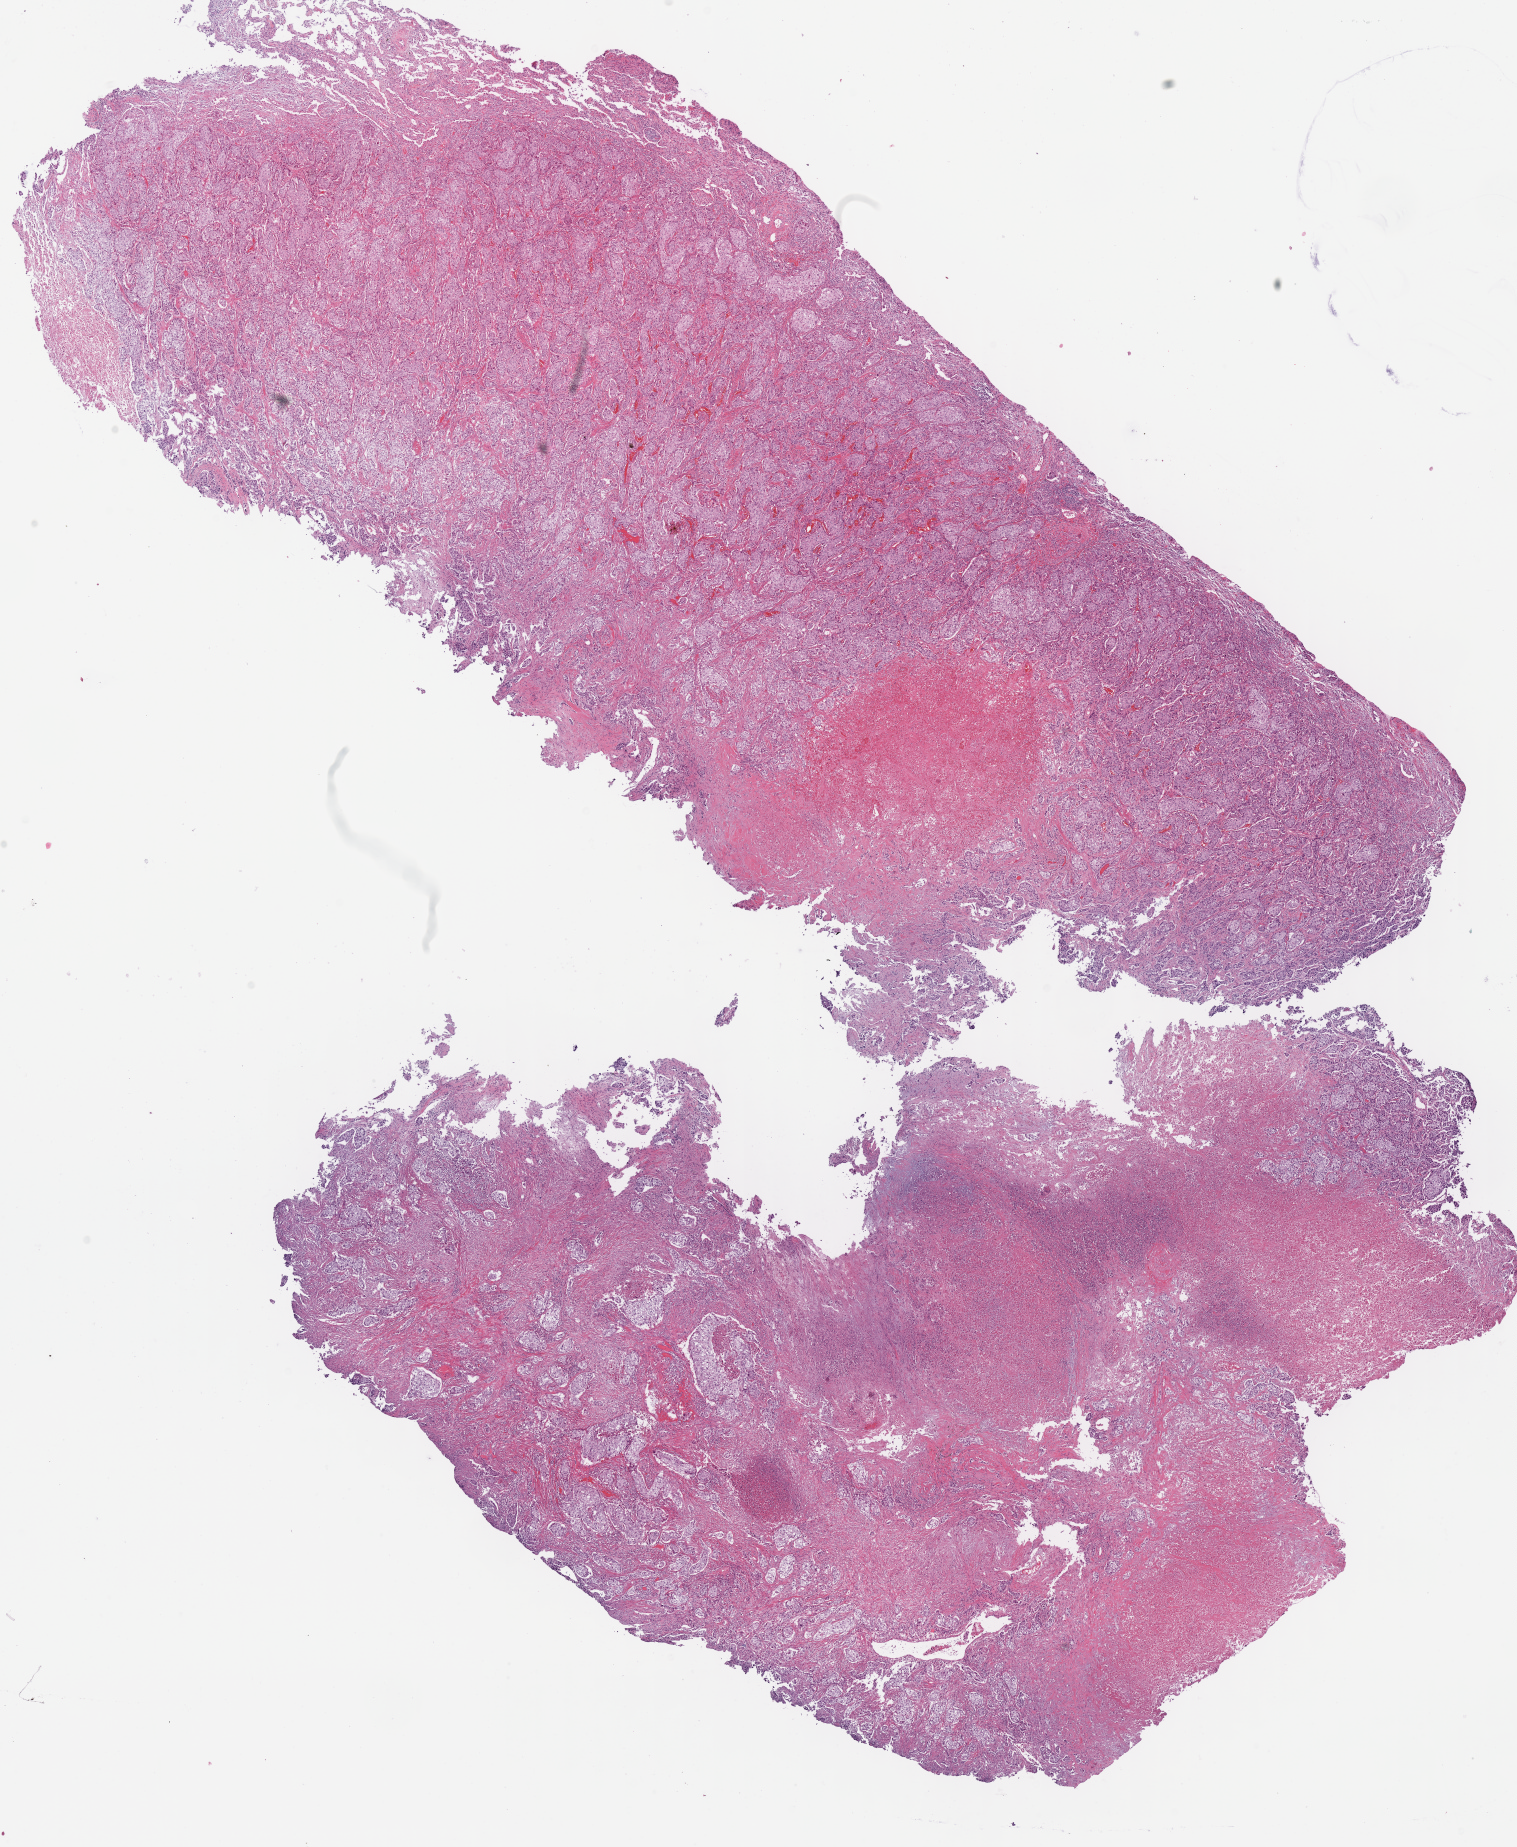
Whole-slide histology image, Hematoxylin and eosin (H&E) stained, a low-resolution overview of the entire scanned area, about 12.0 x 14.6 mm (acquisition: 40x scan), frozen section, lung, primary tumour sample. Male, age 73 years at initial diagnosis. Slide review estimates, as recorded: tumour cells 67%, tumour nuclei 75%, normal cells 3%, stromal cells 15%, necrosis 15%.
AJCC pathologic stage: IB (7th edition). Laterality: right. Pathologic diagnosis: Squamous cell carcinoma, NOS (upper lobe, lung).